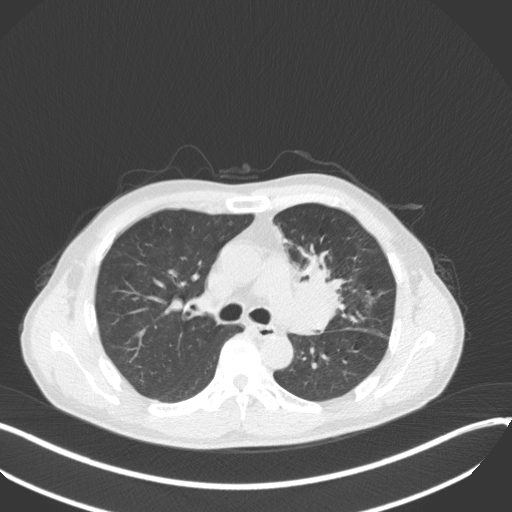
Chest CT, one axial slice; slice 213 of 411 in the series (ordered by position); reconstruction kernel B31f; 120 kVp; lung window (W 1500 / L -600 HU); 512 × 512 image matrix. Male patient, age 56 years. Case-level facts recorded for this patient, not image findings: clinical TNM (as recorded): T2a N0 M0.
Structures marked on this image (bounding box drawn by a radiologist):
- lung tumour (recorded histology: squamous cell carcinoma): bounding box [x1, y1, x2, y2] px = [287, 247, 348, 342]